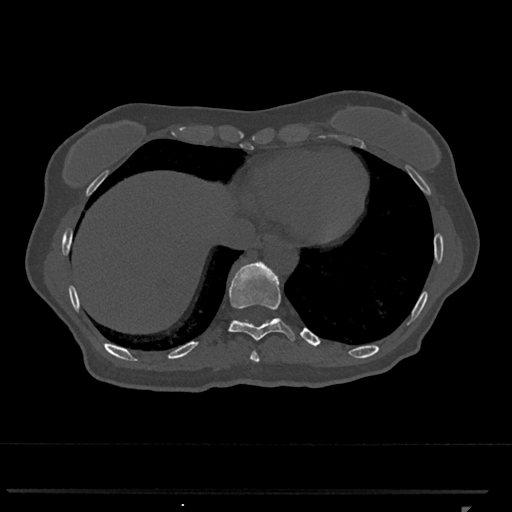
CT including the spine, one axial slice; position 567 of 793 along the scan axis; bone window (W 1800 / L 400 HU); 0.5 mm slice thickness; 512 × 512 image matrix, field of view 380 × 380 mm. Female patient, age 62 years. Case-level facts recorded for this patient, not image findings: primary cancer: renal.
Annotated regions visible in this slice (semi-automatic segmentation, software-assisted and operator-edited):
- T10 vertebra: bounding box (x1, y1, x2, y2) in pixels: (228, 261, 295, 341)
- T11 vertebra: (235, 308, 271, 320)
- T9 vertebra: (250, 351, 259, 362)